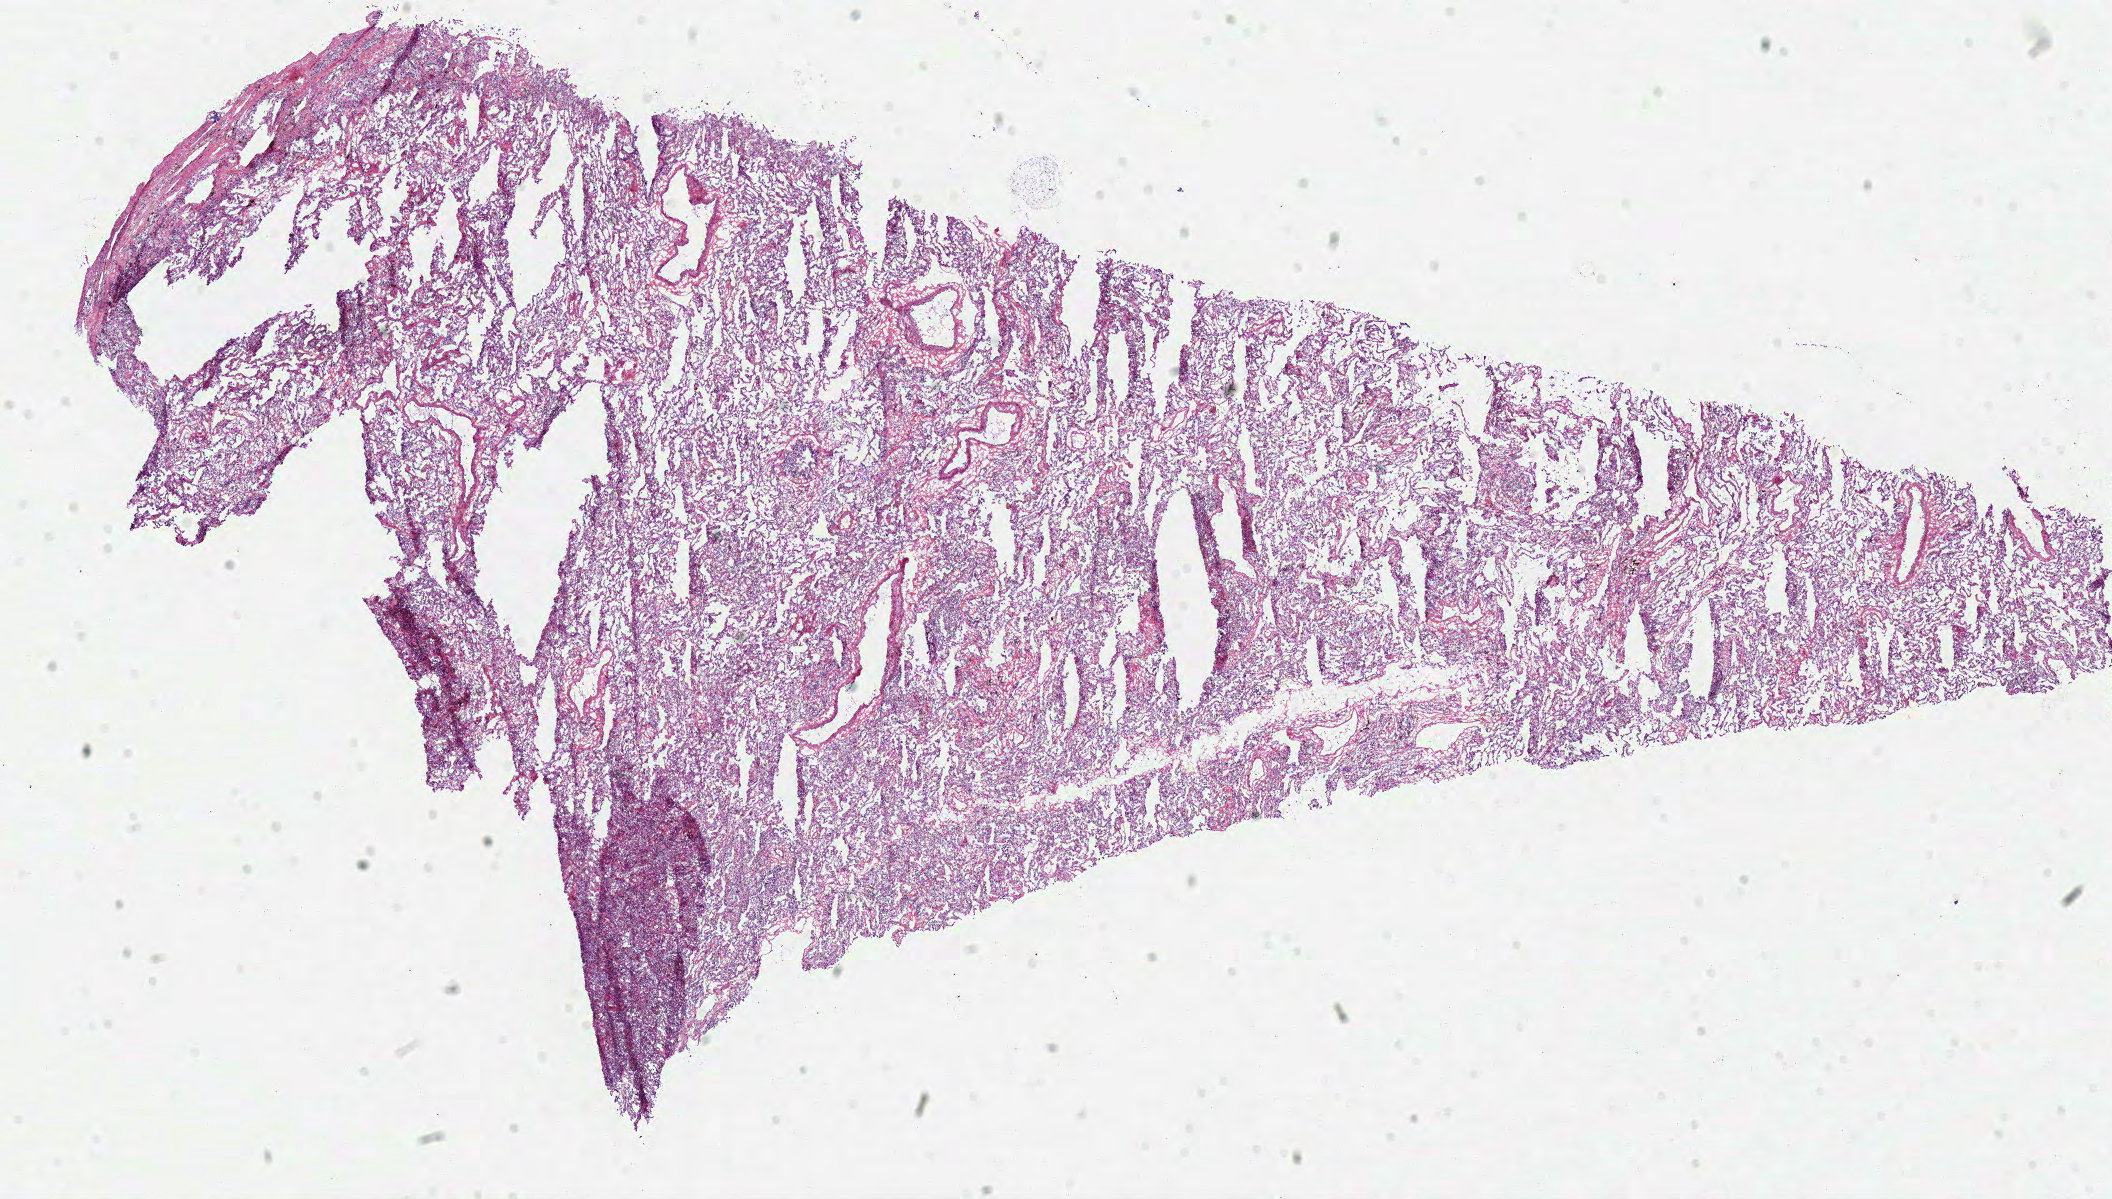
Digitized H&E tissue section (whole slide) — whole scanned area (about 16.6 x 9.4 mm) shown as a low-resolution overview. Frozen section from the top of the tissue portion. Solid tissue normal (non-tumour tissue) sample from the lung. Female patient; age at initial diagnosis 49 years.
• this section: solid tissue normal sample (biorepository sample class)
• patient diagnosis: Adenocarcinoma with mixed subtypes (upper lobe, lung)